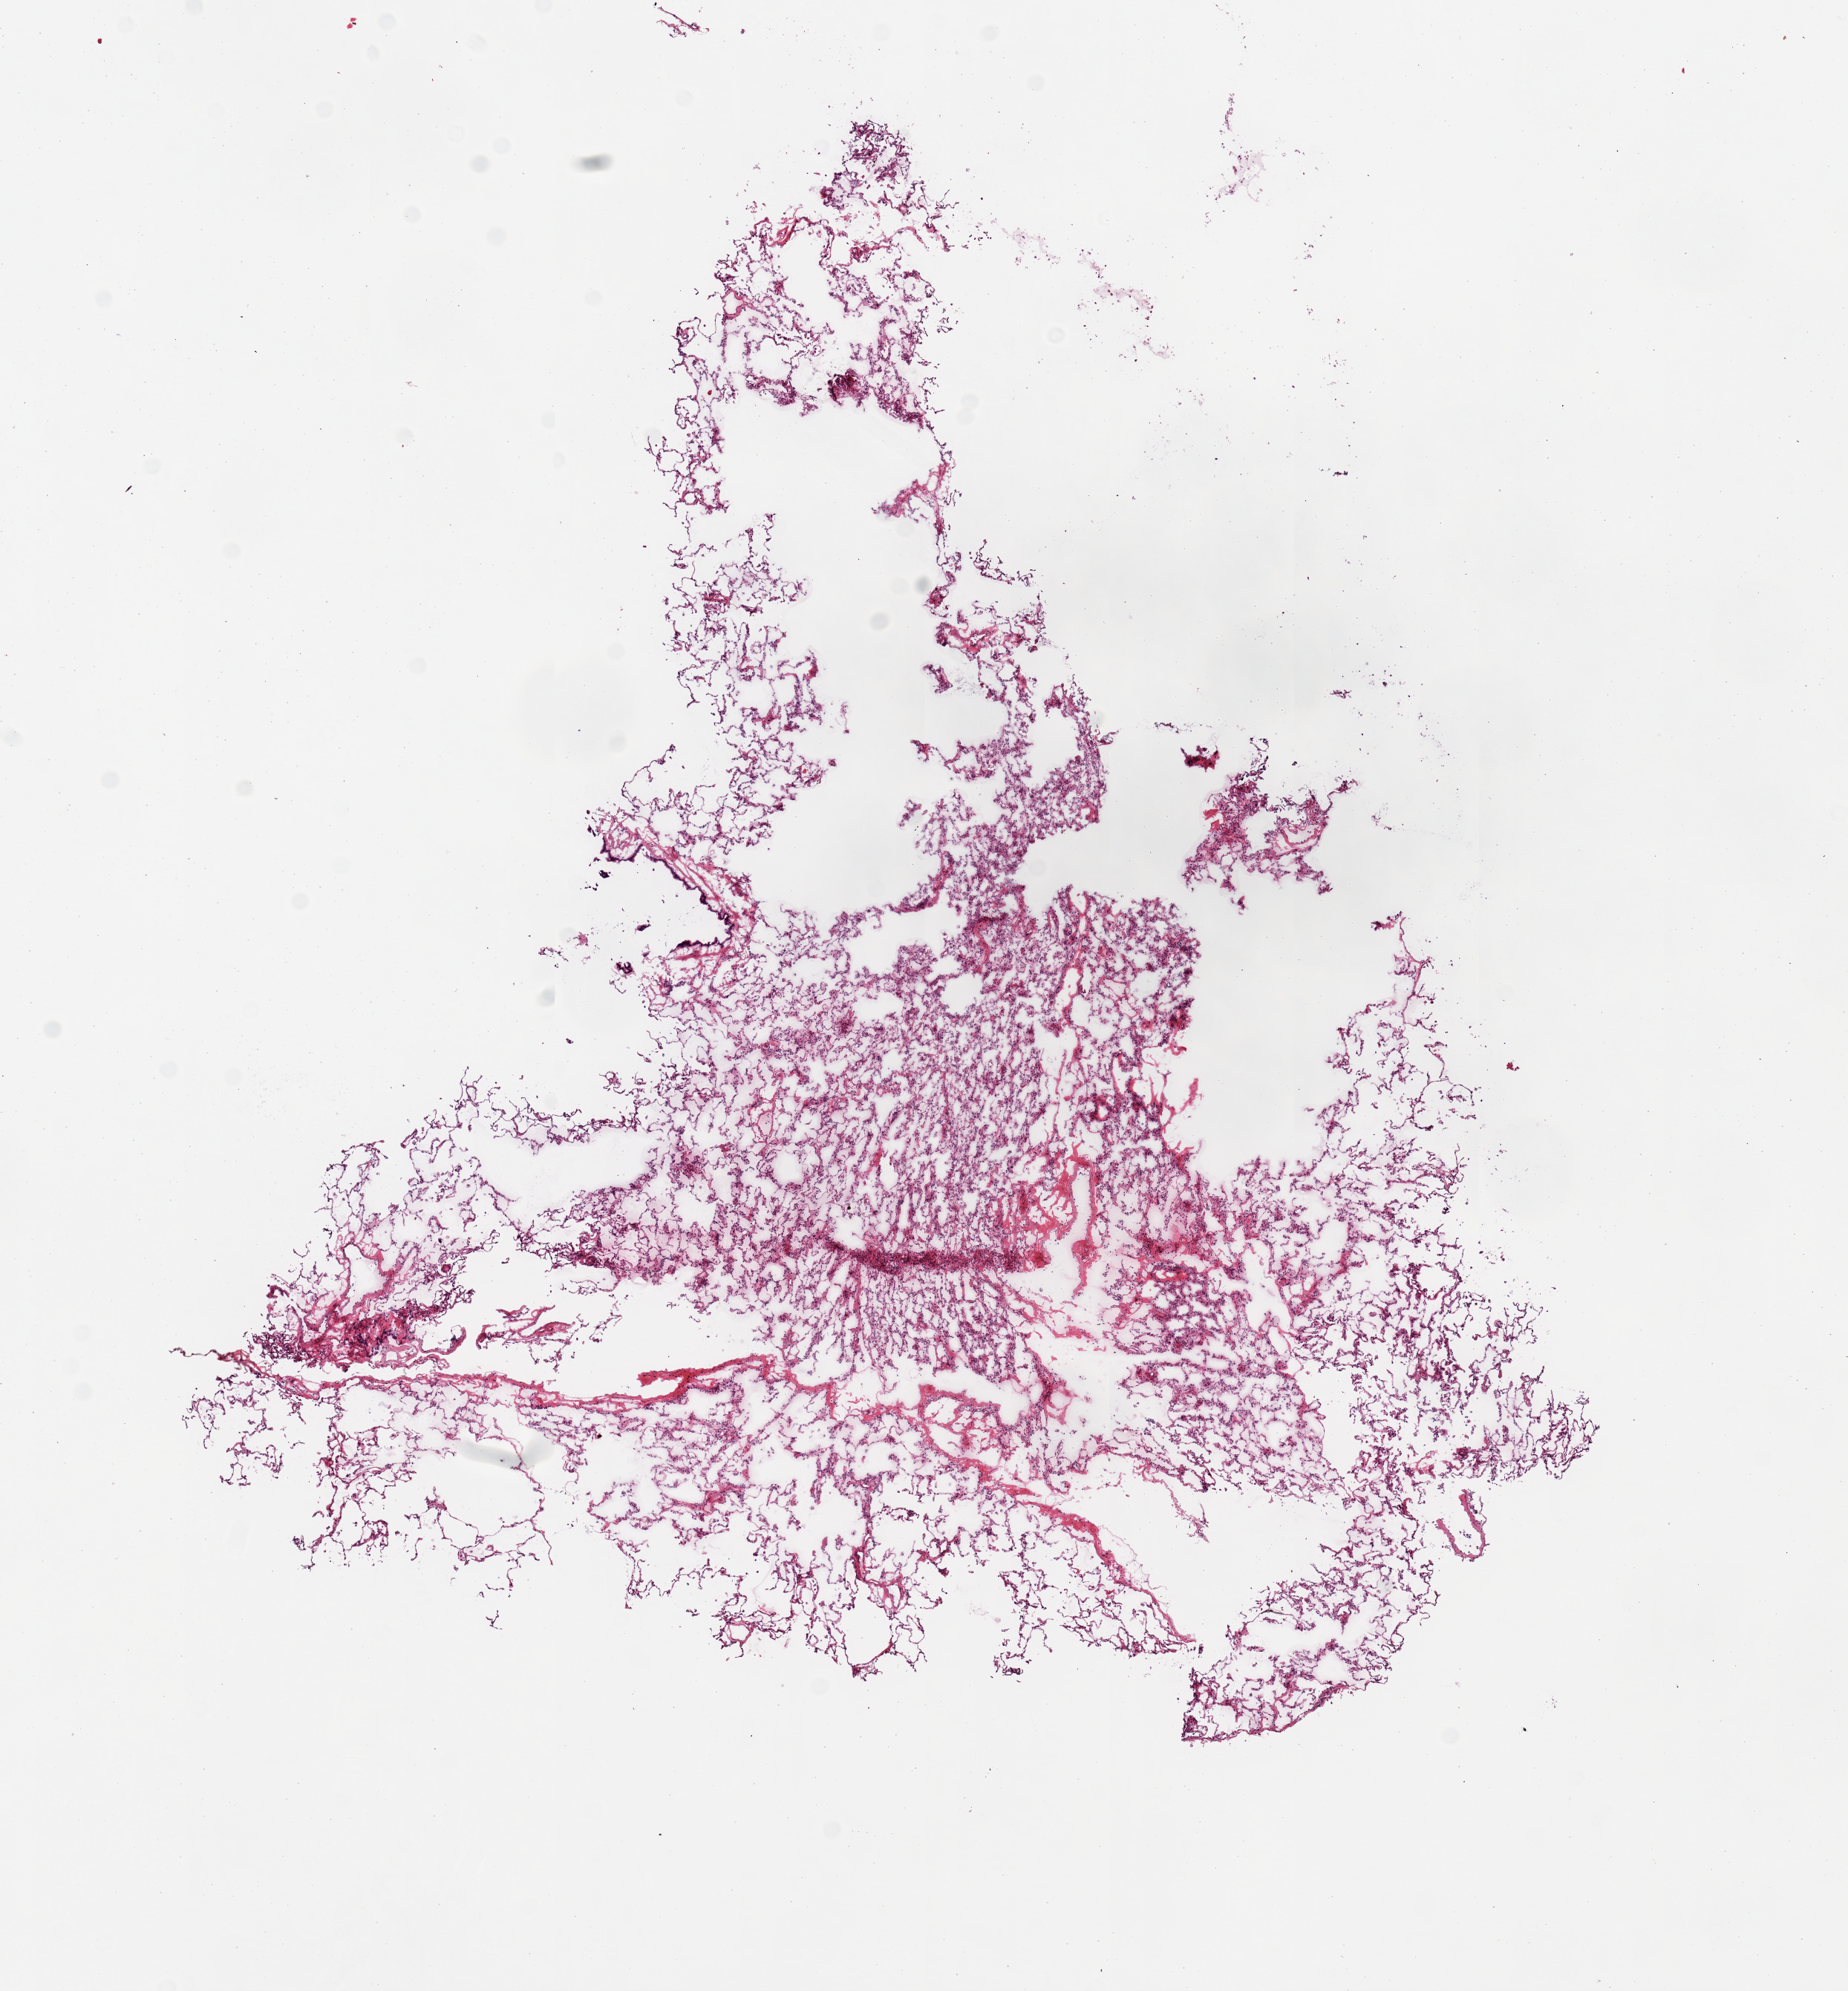
H&E whole-slide image, whole scanned area (about 9.8 x 10.6 mm, slide scanned at 20x) shown as a low-resolution overview, frozen section (dry ice), section of lung (target tissue), tissue donor sample.
Review note (as recorded): 1 piece.